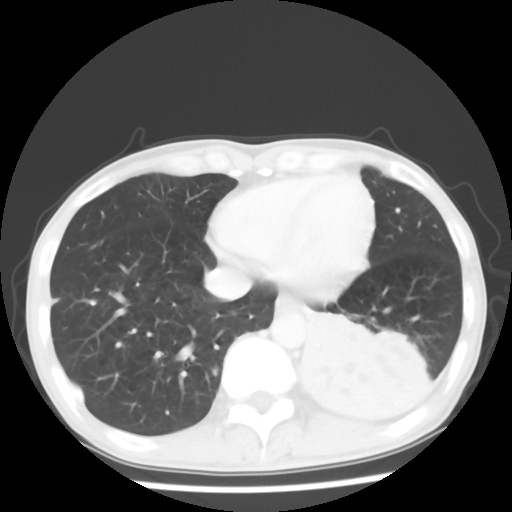
Chest CT, one axial slice; slice 16 of 64 in the series (ordered by position); reconstruction kernel STANDARD; 120 kVp; lung window (W 1500 / L -600 HU); 512 × 512 image matrix, field of view 313 × 313 mm. Male patient, age 68 years. Case-level facts recorded for this patient, not image findings: clinical TNM (as recorded): T4 N0 M0.
Structures marked on this image (bounding box drawn by a radiologist):
- lung tumour (recorded histology: squamous cell carcinoma): bounding box [x1, y1, x2, y2] px = [290, 306, 442, 421]